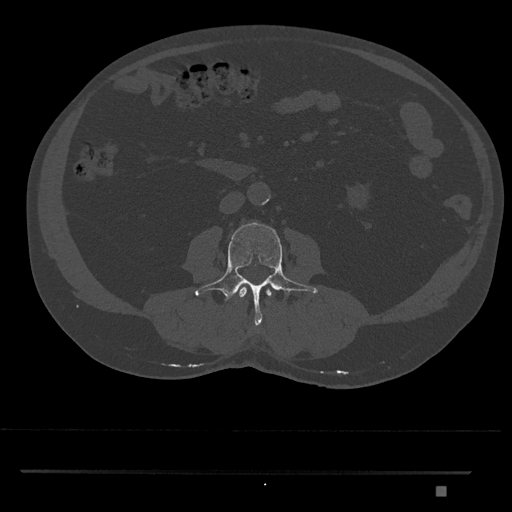
CT including the spine, one axial slice; position 688 of 1134 along the scan axis; reconstruction kernel Br40s/3; 120 kVp; bone window (W 1800 / L 400 HU); 0.5 mm slice thickness; 512 × 512 image matrix, field of view 429 × 429 mm. Male patient, age 65 years. From the clinical record (not read from this slice): primary cancer: prostate.
Outlined on this slice (semi-automatic segmentation, software-assisted and operator-edited):
- L2 vertebra: bounding box (x1, y1, x2, y2) in pixels: (239, 284, 272, 299)
- L3 vertebra: (195, 222, 318, 327)